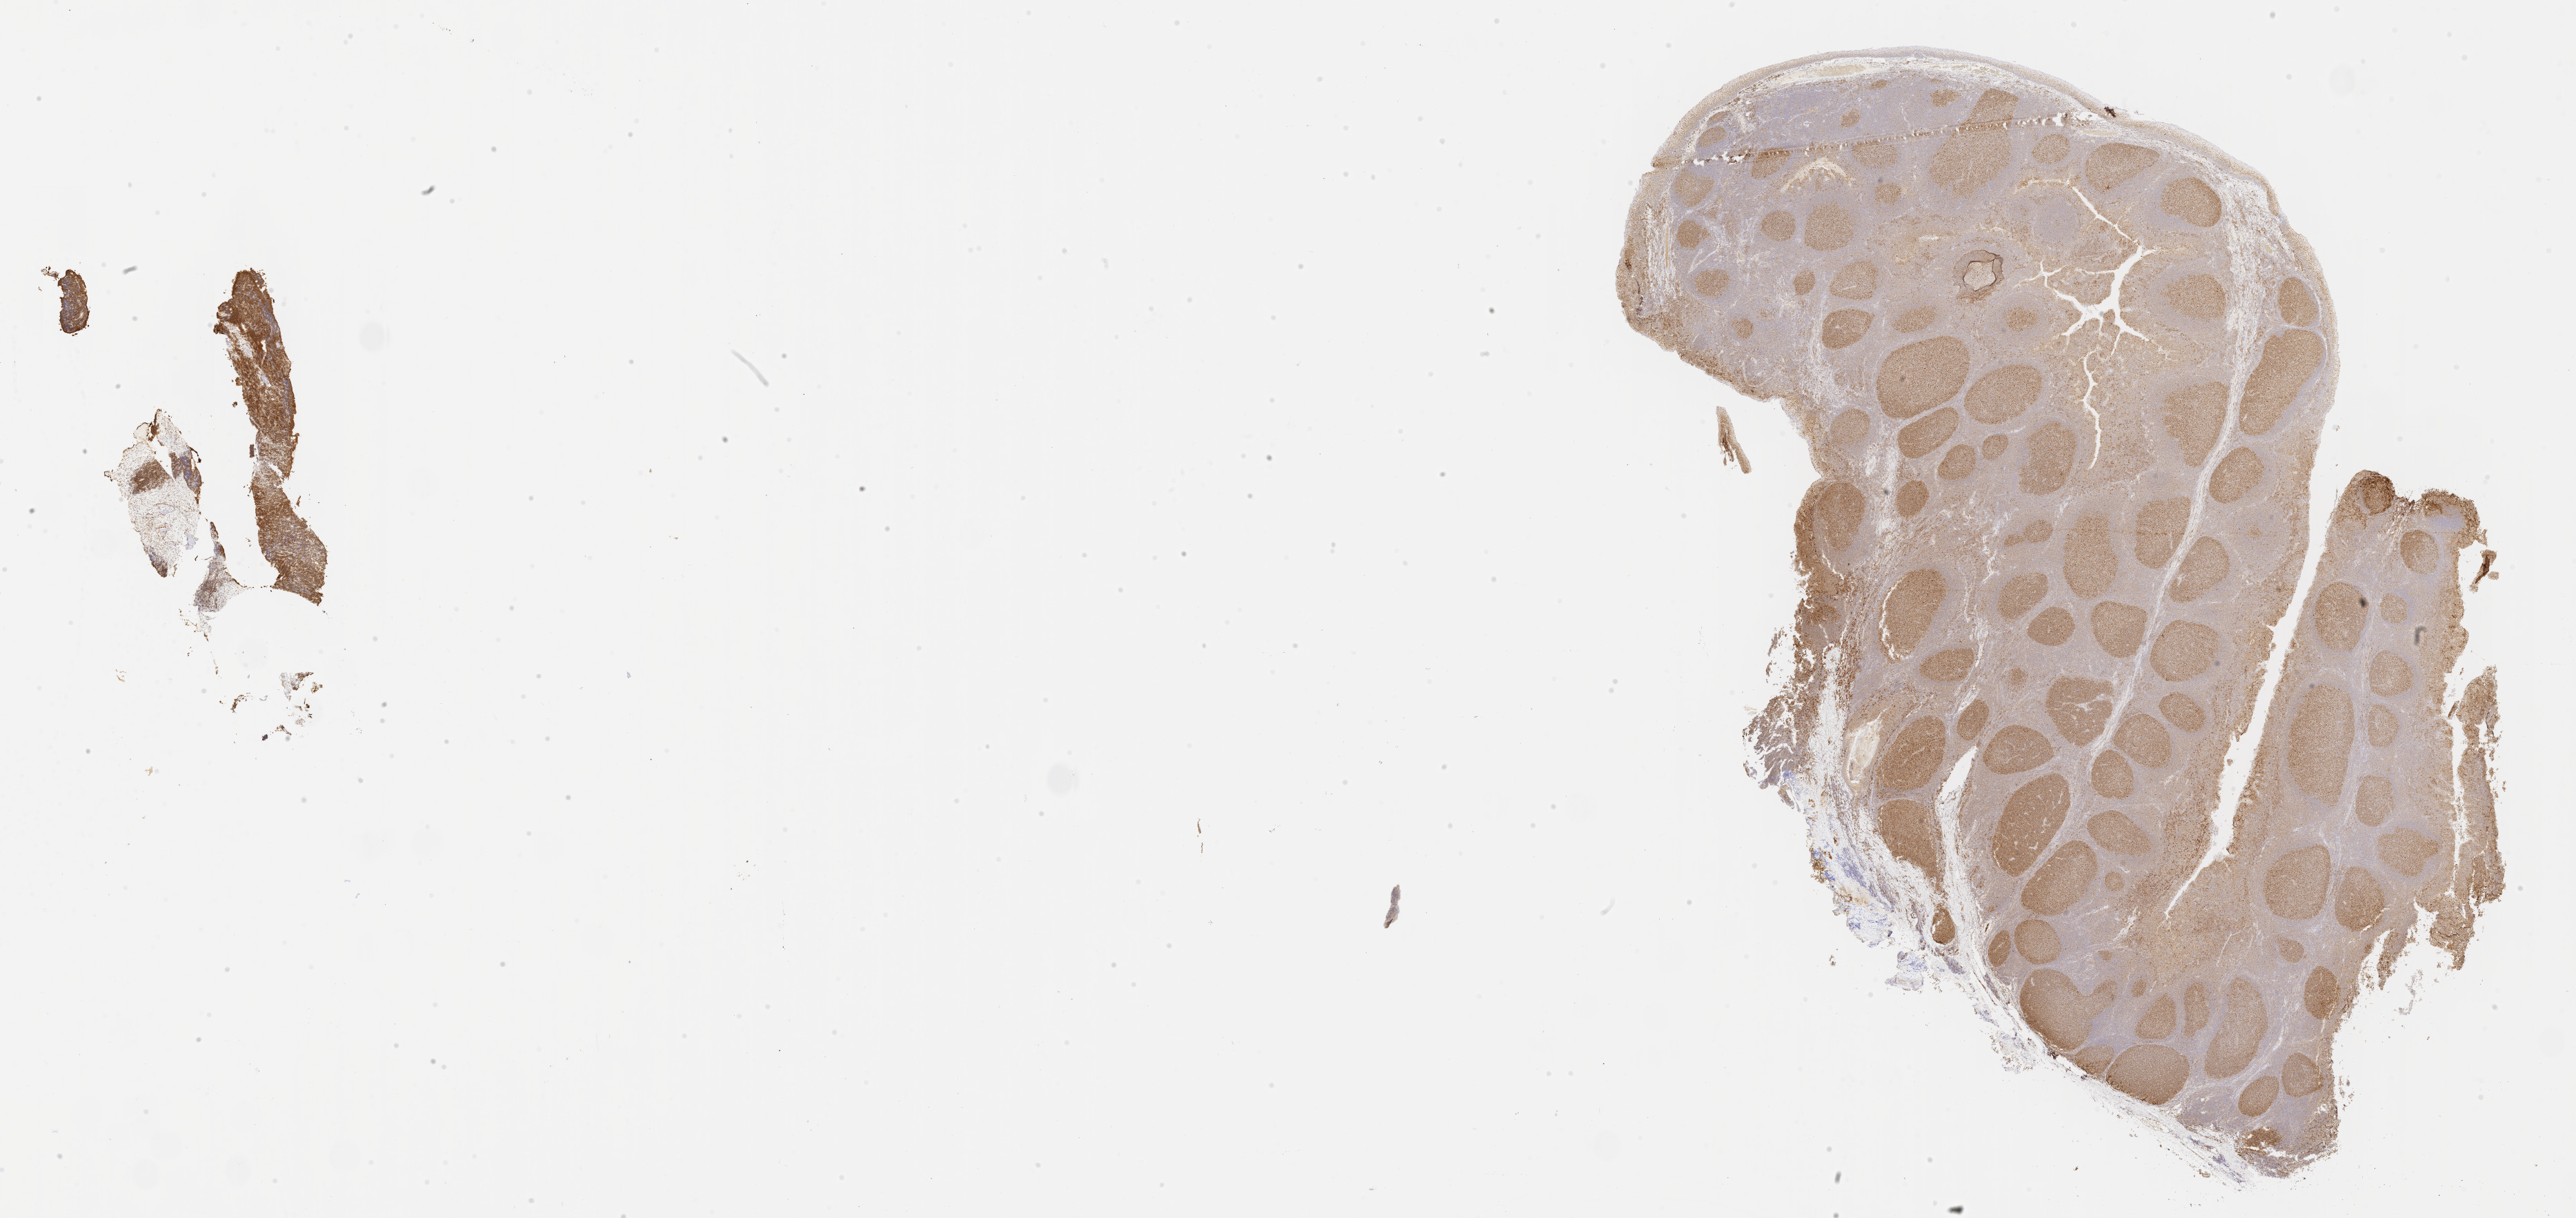
IHC for BCL6, whole-slide image, whole scanned area (about 30.2 x 14.3 mm) shown as a low-resolution overview. Tumor tissue. Site: mandible. Male, age 6 years at initial diagnosis.
Diagnosis: Burkitt lymphoma, NOS.